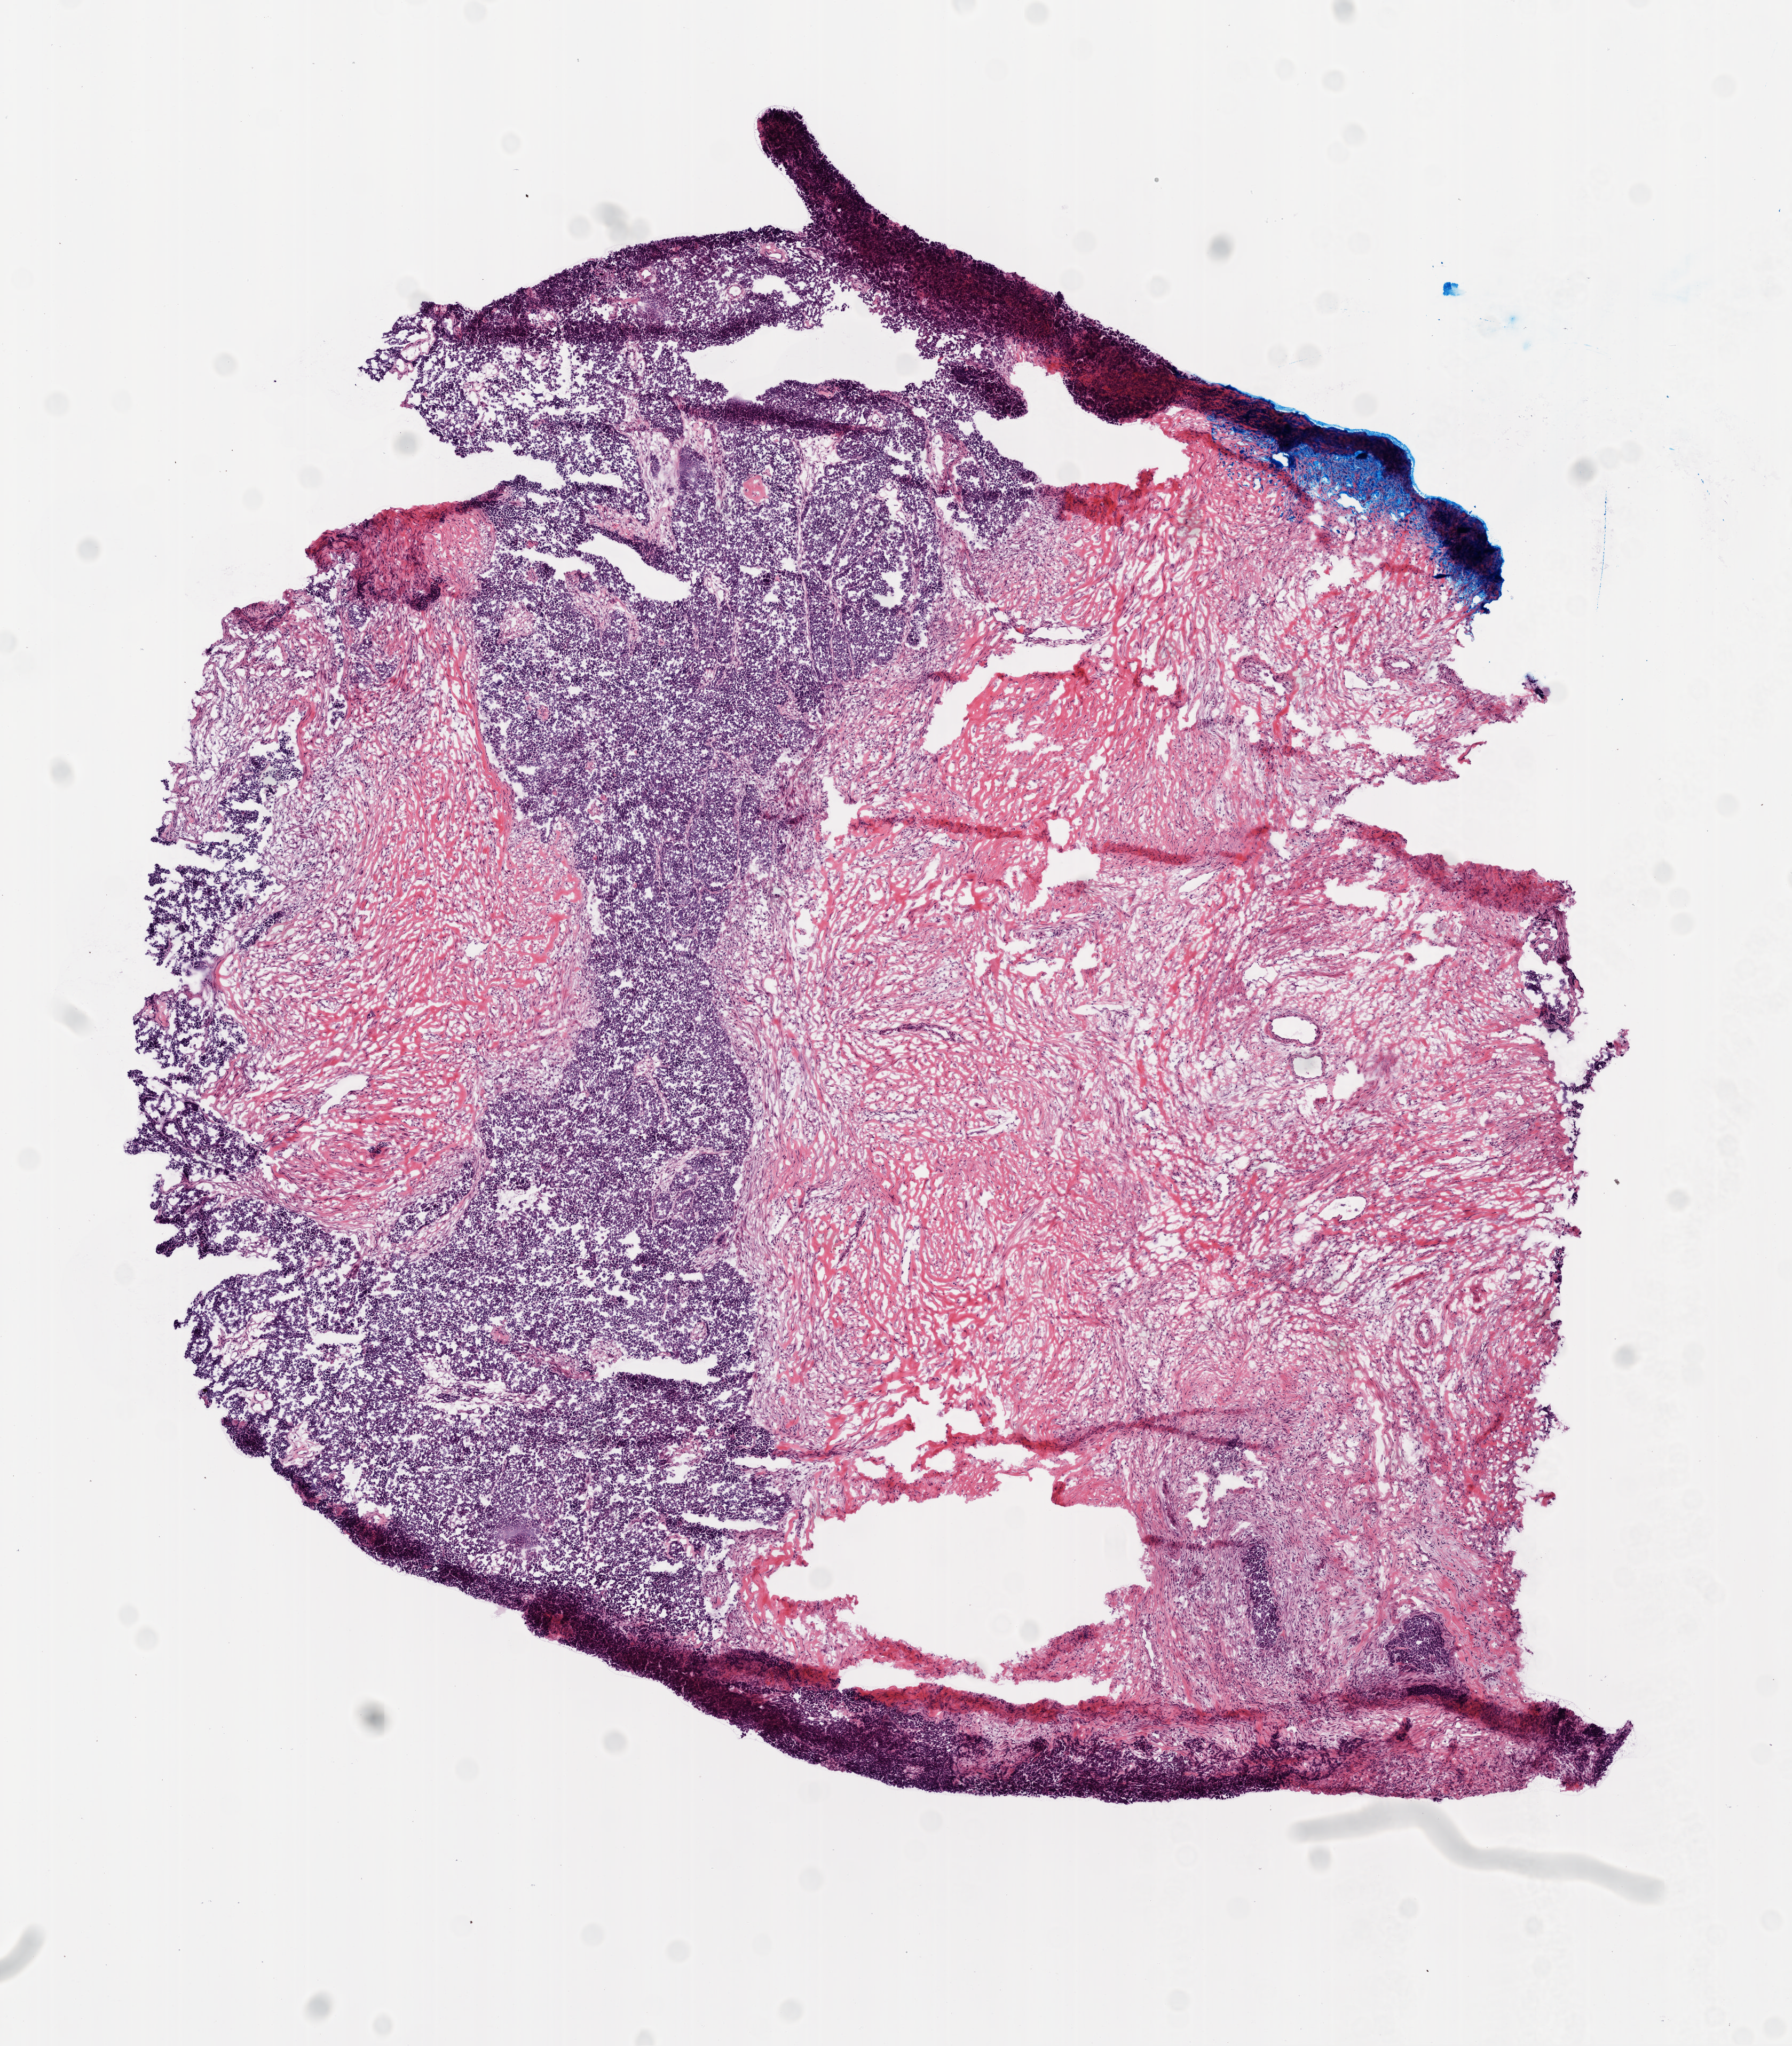
Hematoxylin and eosin (H&E) stained whole-slide image — shown as a low-resolution overview of the whole scanned area (about 6.8 x 7.7 mm, acquisition: 20x scan), frozen section from the top of the tissue portion, ovary, primary tumour sample. Female, age 62 years at initial diagnosis. Histologic grade: G3 (poorly differentiated). Composition of this section per pathologist review: tumour nuclei 90%, normal cells 0%, necrosis 0%.
FIGO stage: IIIC. Pathologic diagnosis: Serous cystadenocarcinoma, NOS.